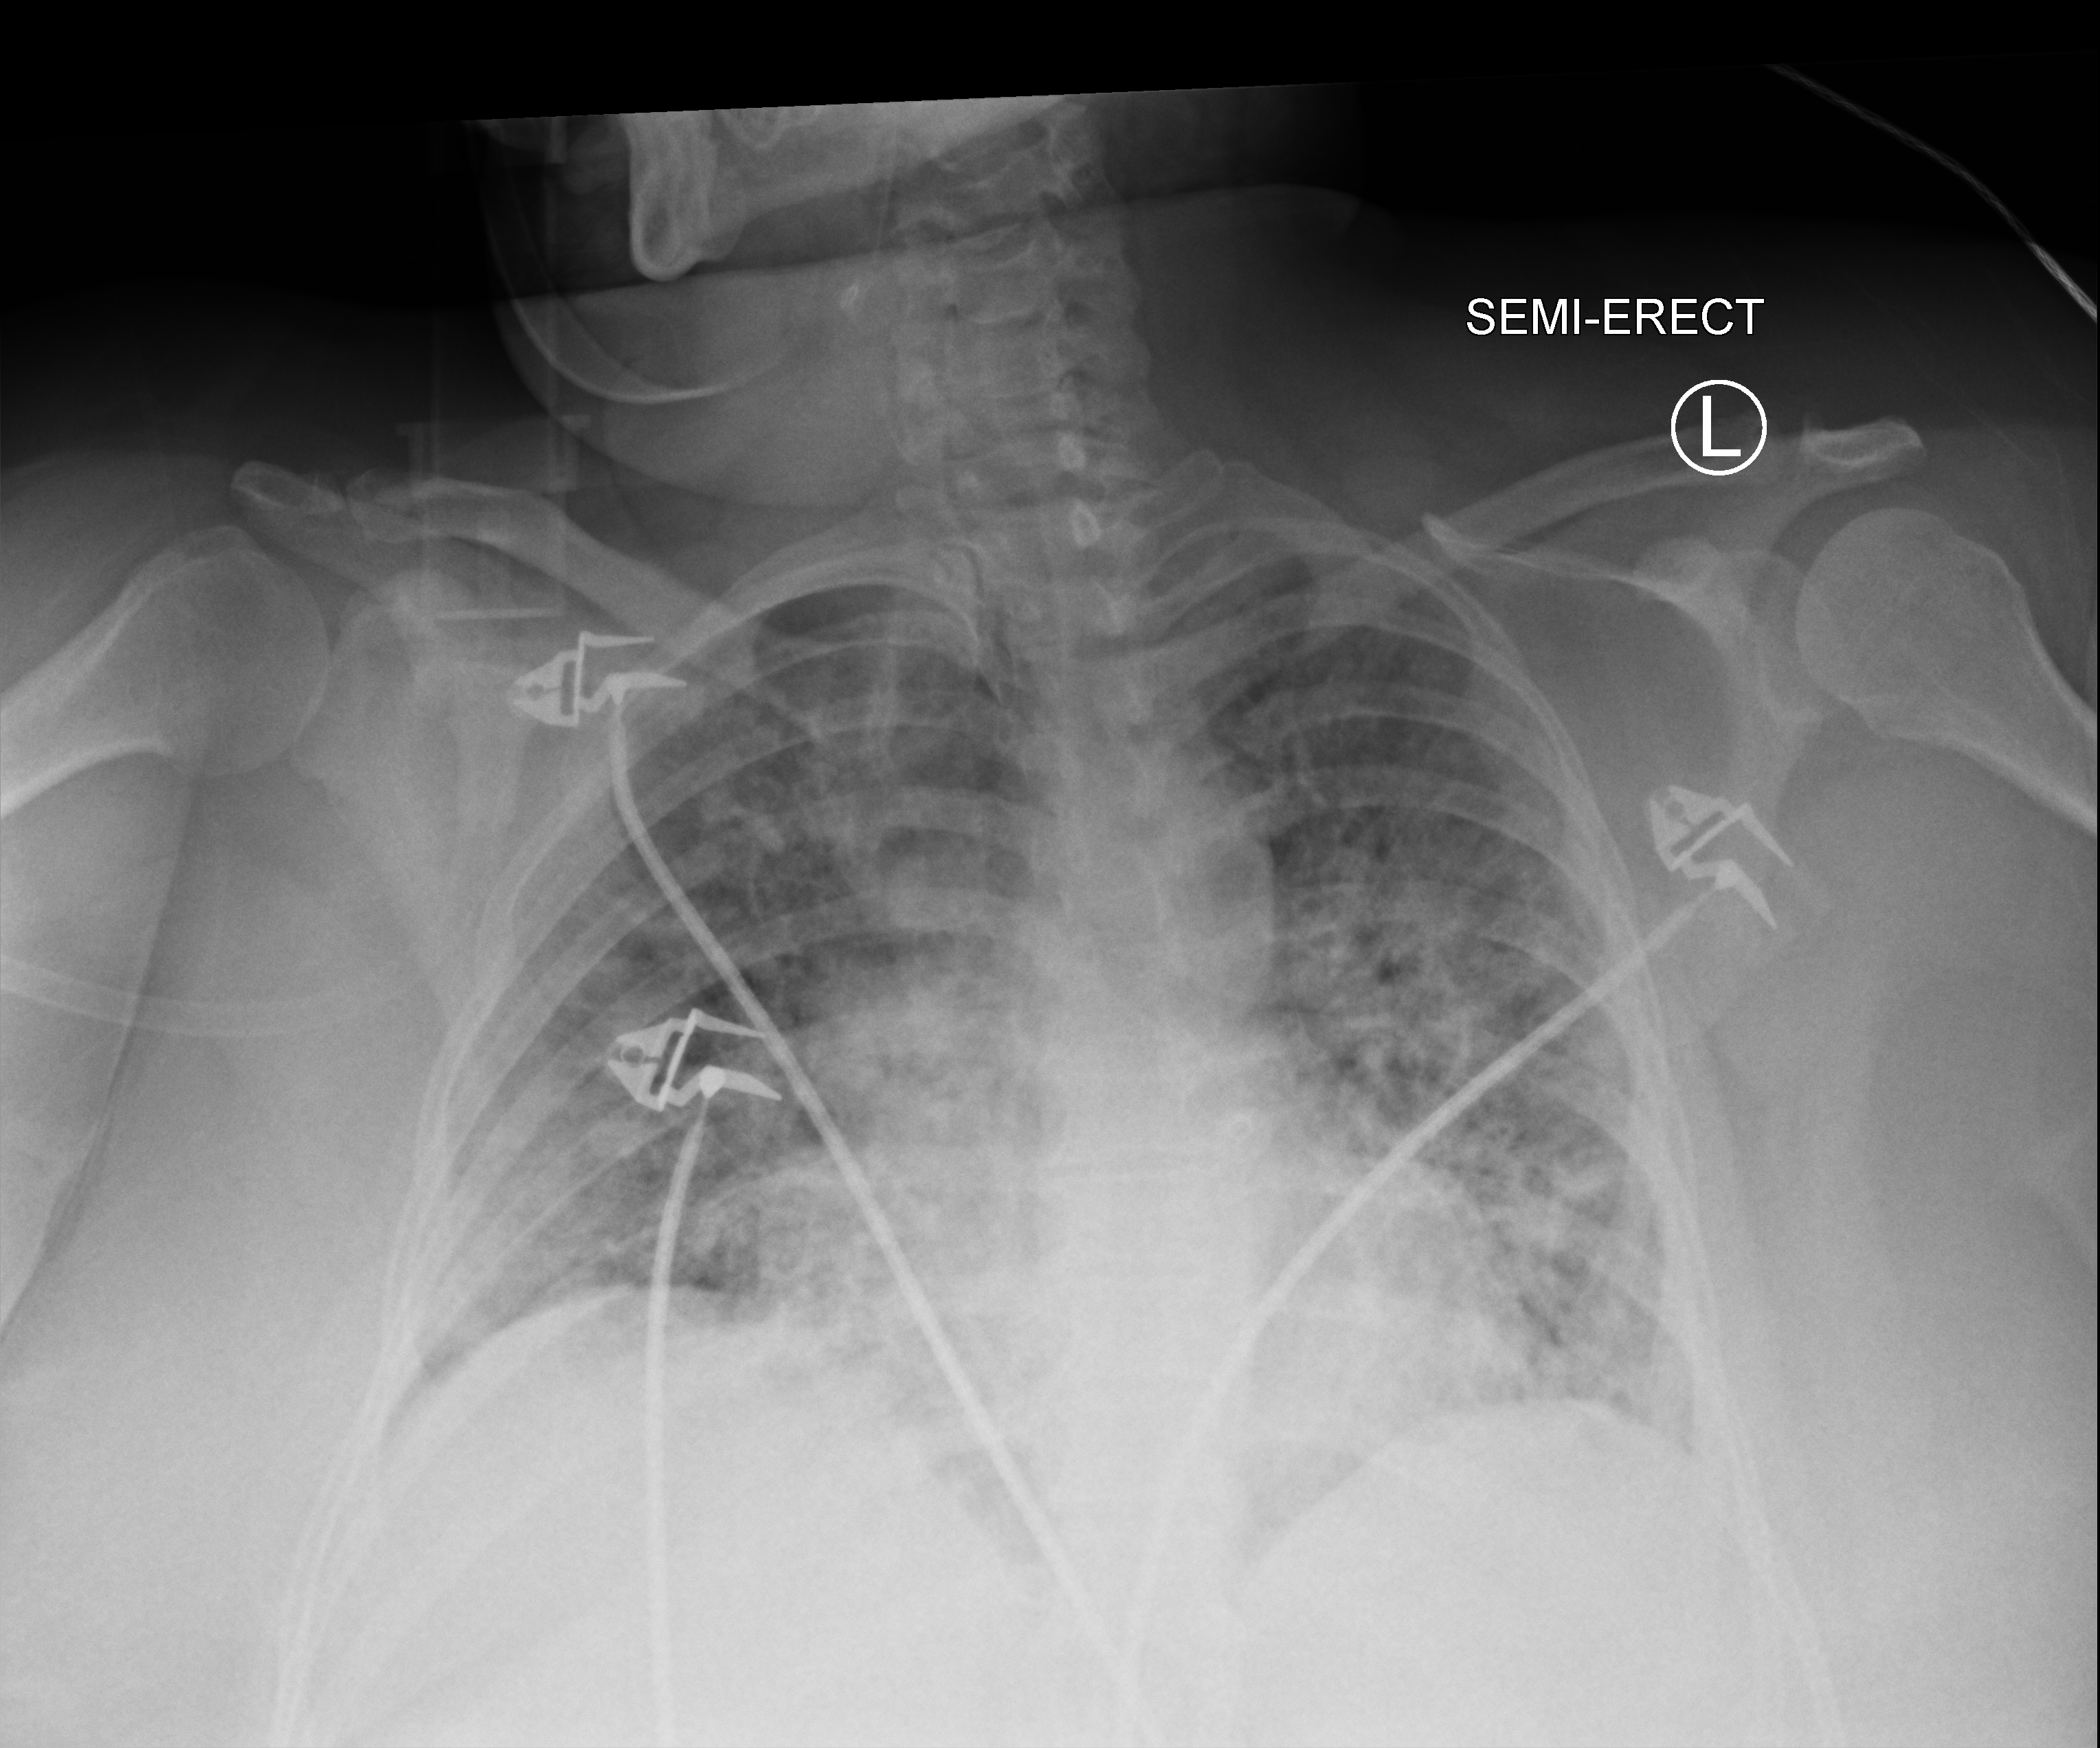
Chest X-ray (portable). Female patient hospitalised with COVID-19, age 18–59 years.
Admission-level facts for this patient (not findings on this image; timing relative to this image not recorded):
- mechanically ventilated during this hospital stay: yes
- other chronic lung disease (admission record): no